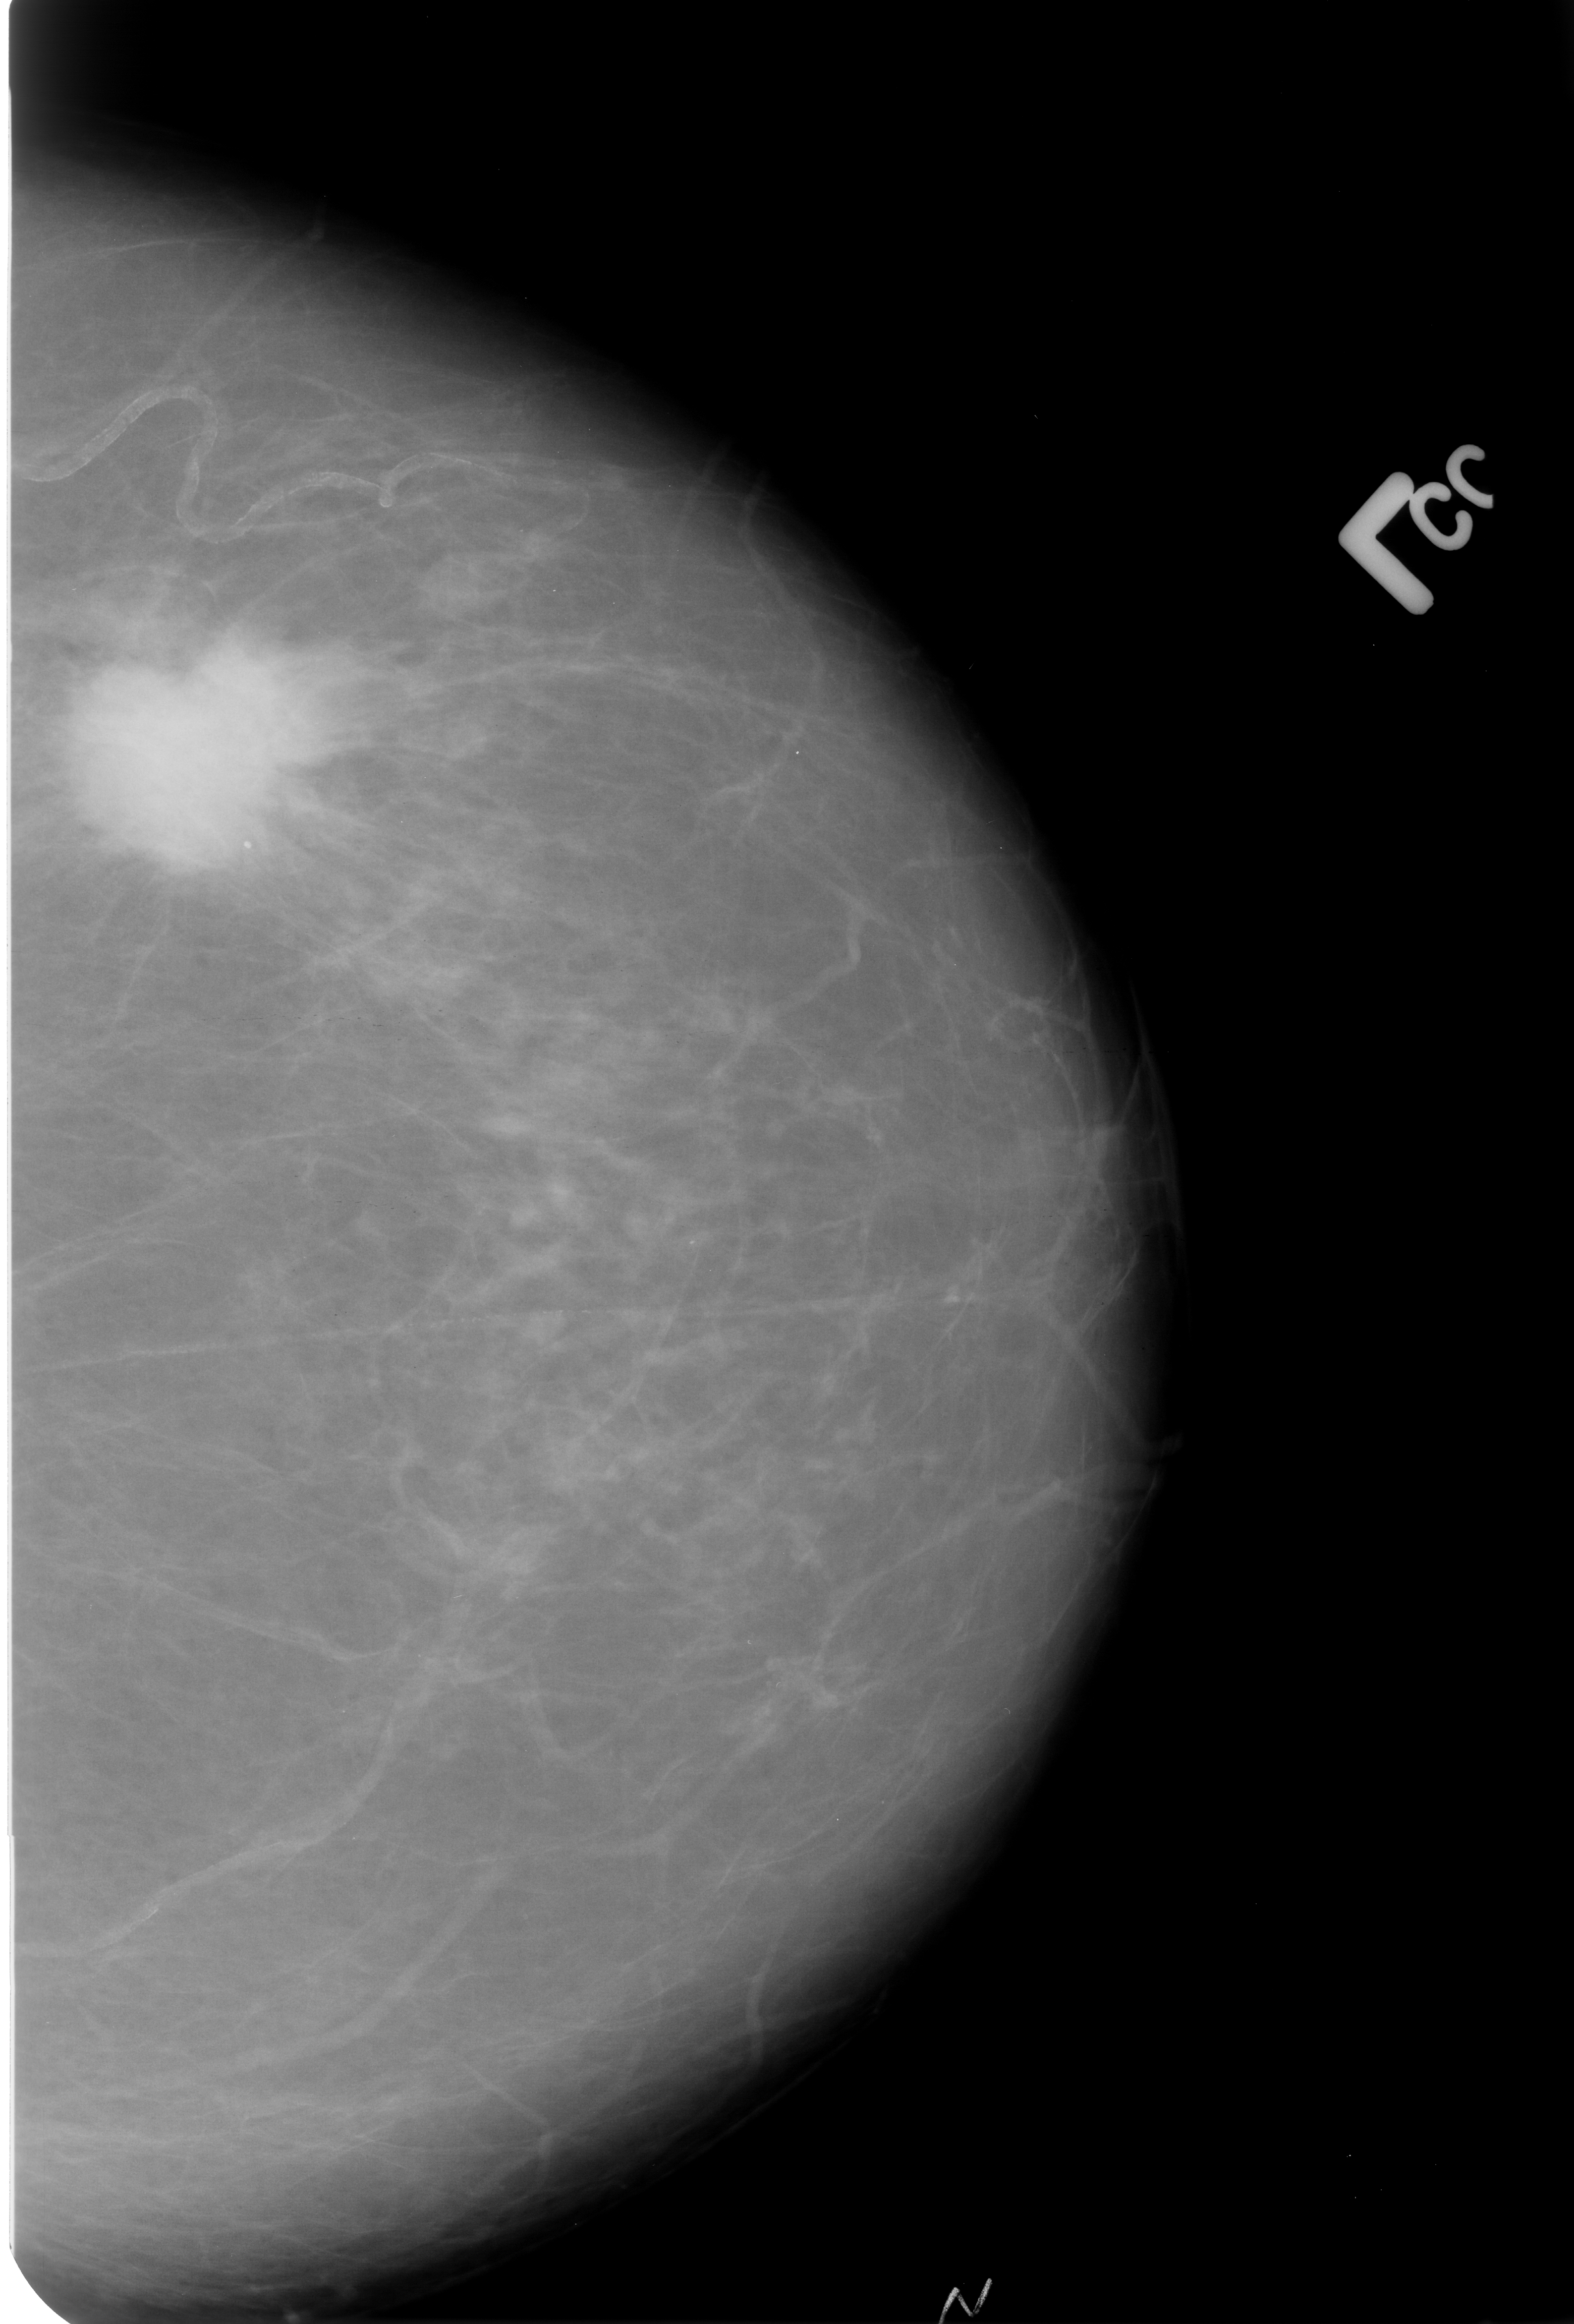
Digitized screen-film mammogram, left breast, CC view, BI-RADS breast density category 2 (scale 1–4).
- Mass, shape round / irregular / architectural distortion, margins spiculated; BI-RADS assessment category 5; subtlety rating 5 on a 1 (subtle) to 5 (obvious) scale; pathology (as recorded): malignant.